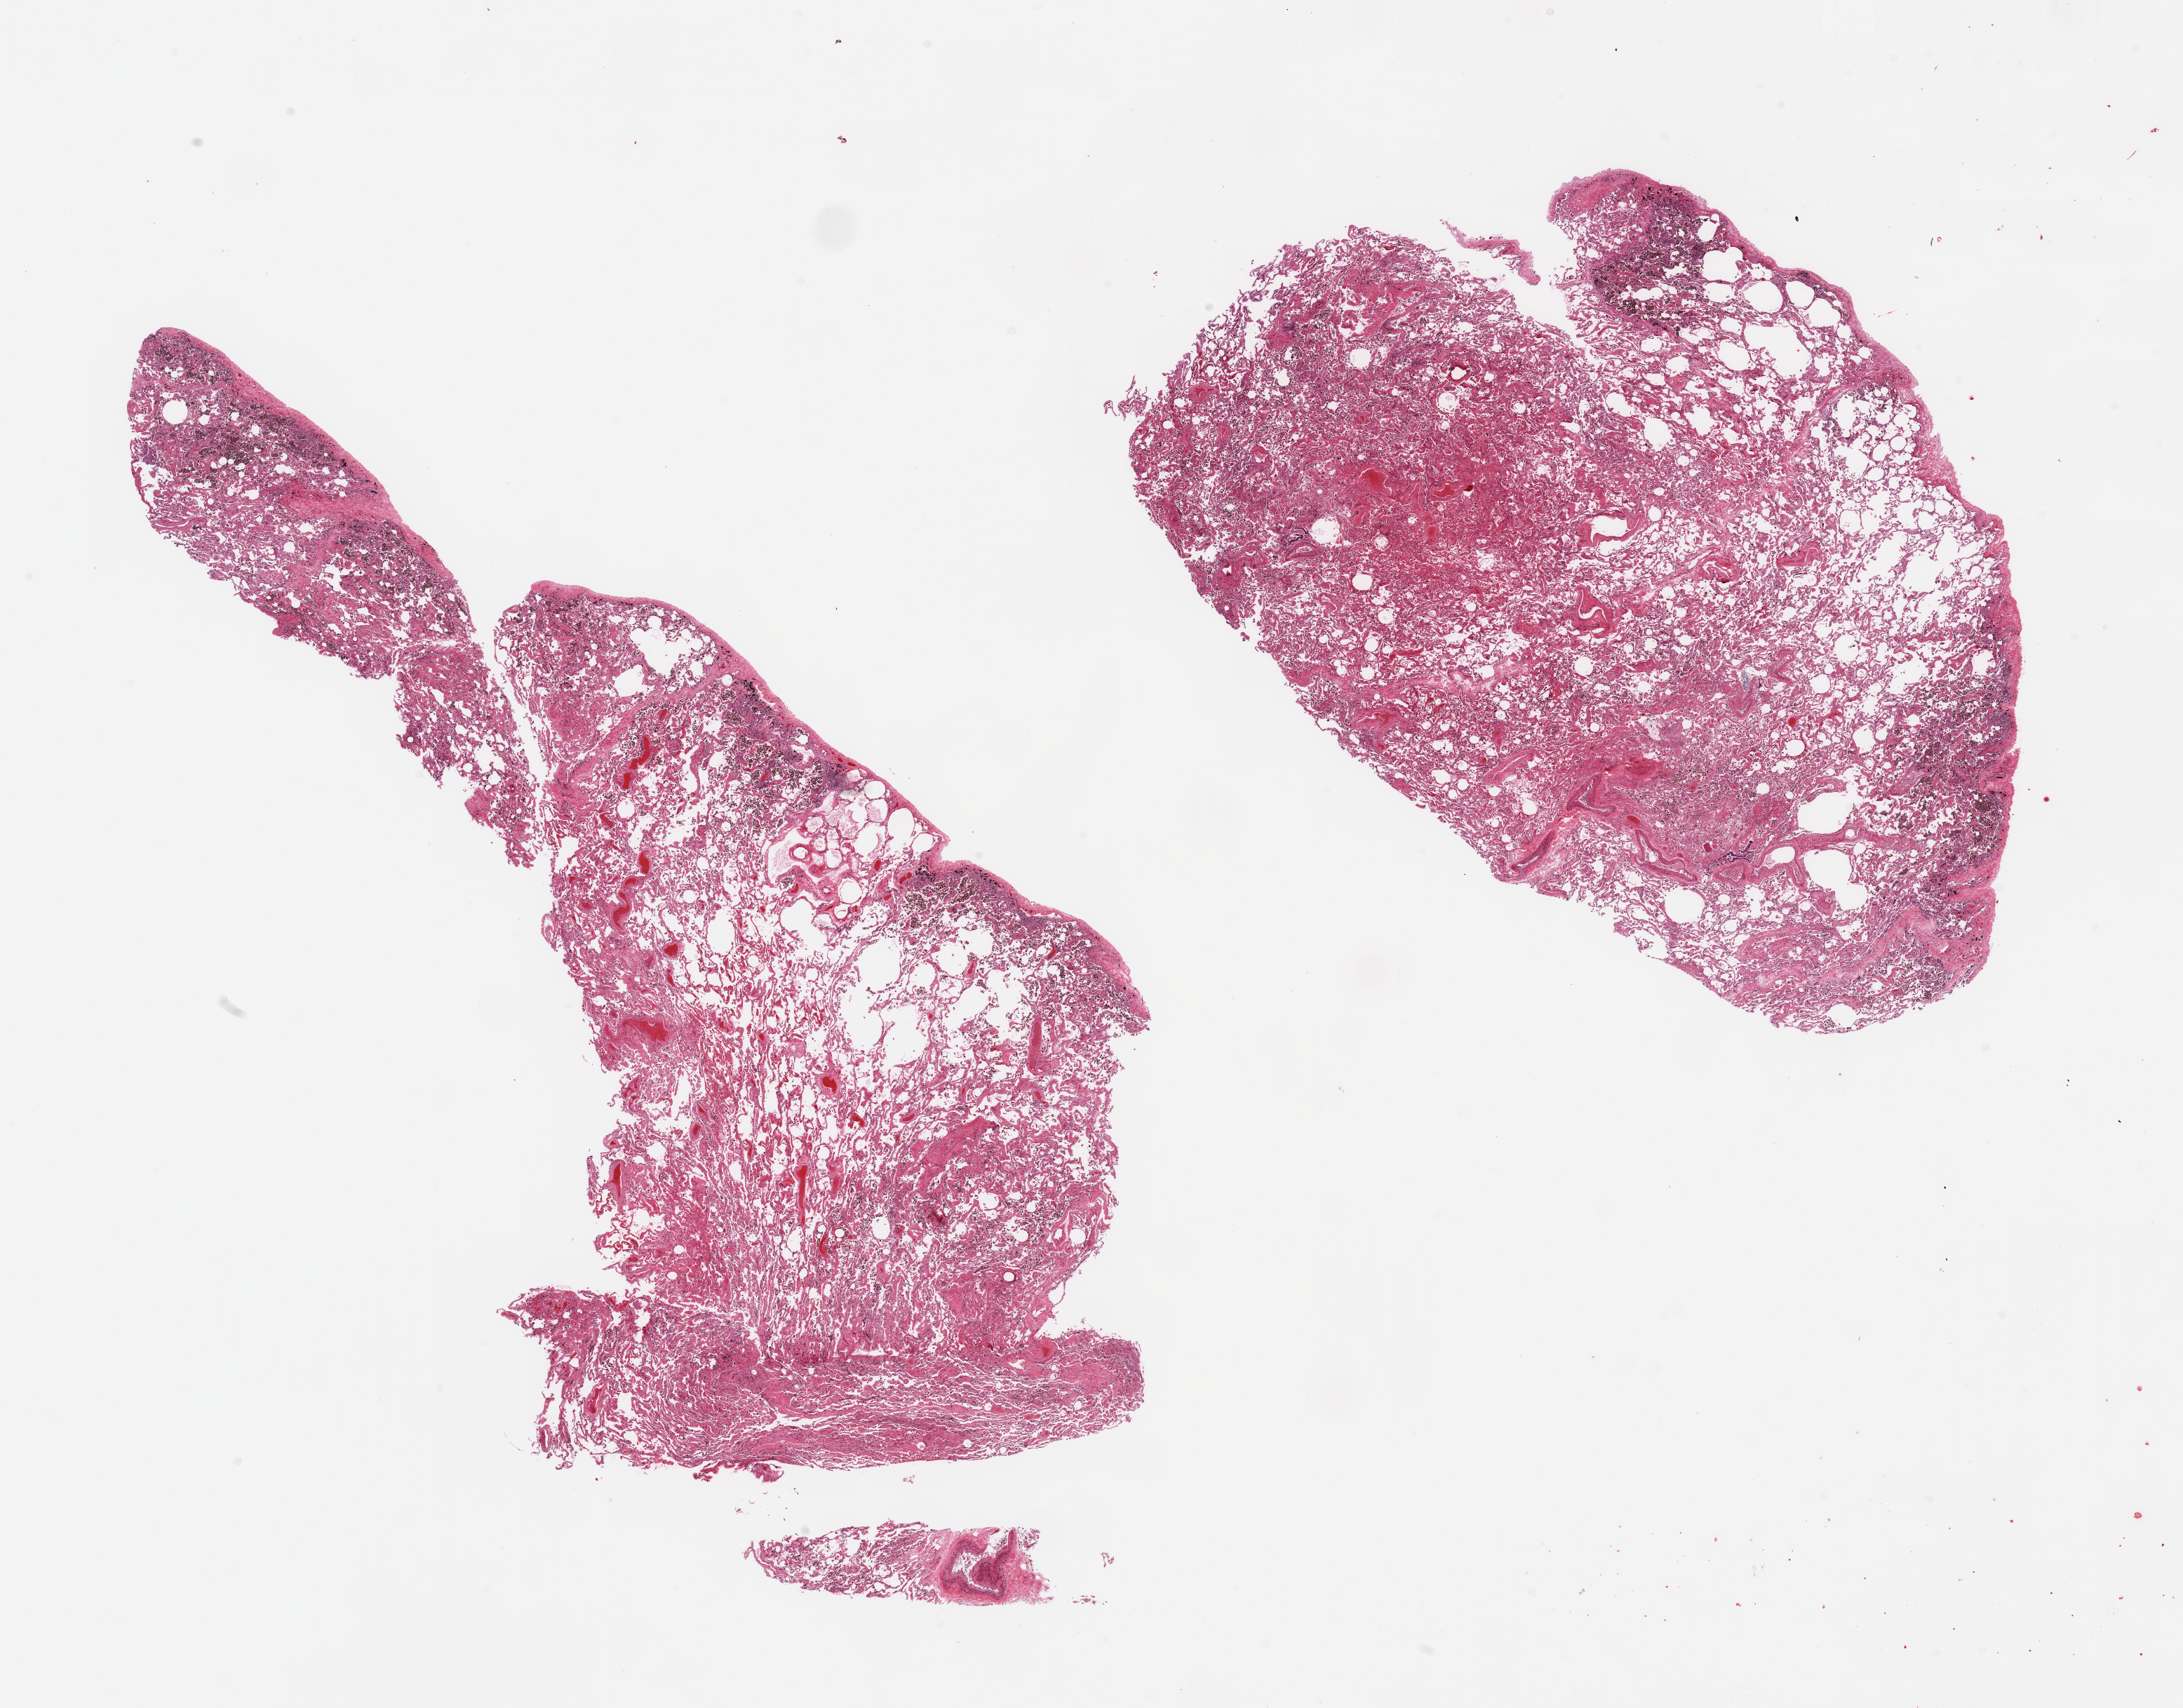
Whole-slide image, hematoxylin and eosin (H&E) stain — whole scanned area (about 24.6 x 19.3 mm, from a 20x scan) shown as a low-resolution overview. PAXgene-fixed, paraffin-embedded tissue. Target tissue: lung. Tissue donor sample. Female donor.
Pathologist's review note for this sample: 2 pieces; include pleura (target is 1cm below pleura), numerous pigmented macrophages, some congestion, fibrosis.